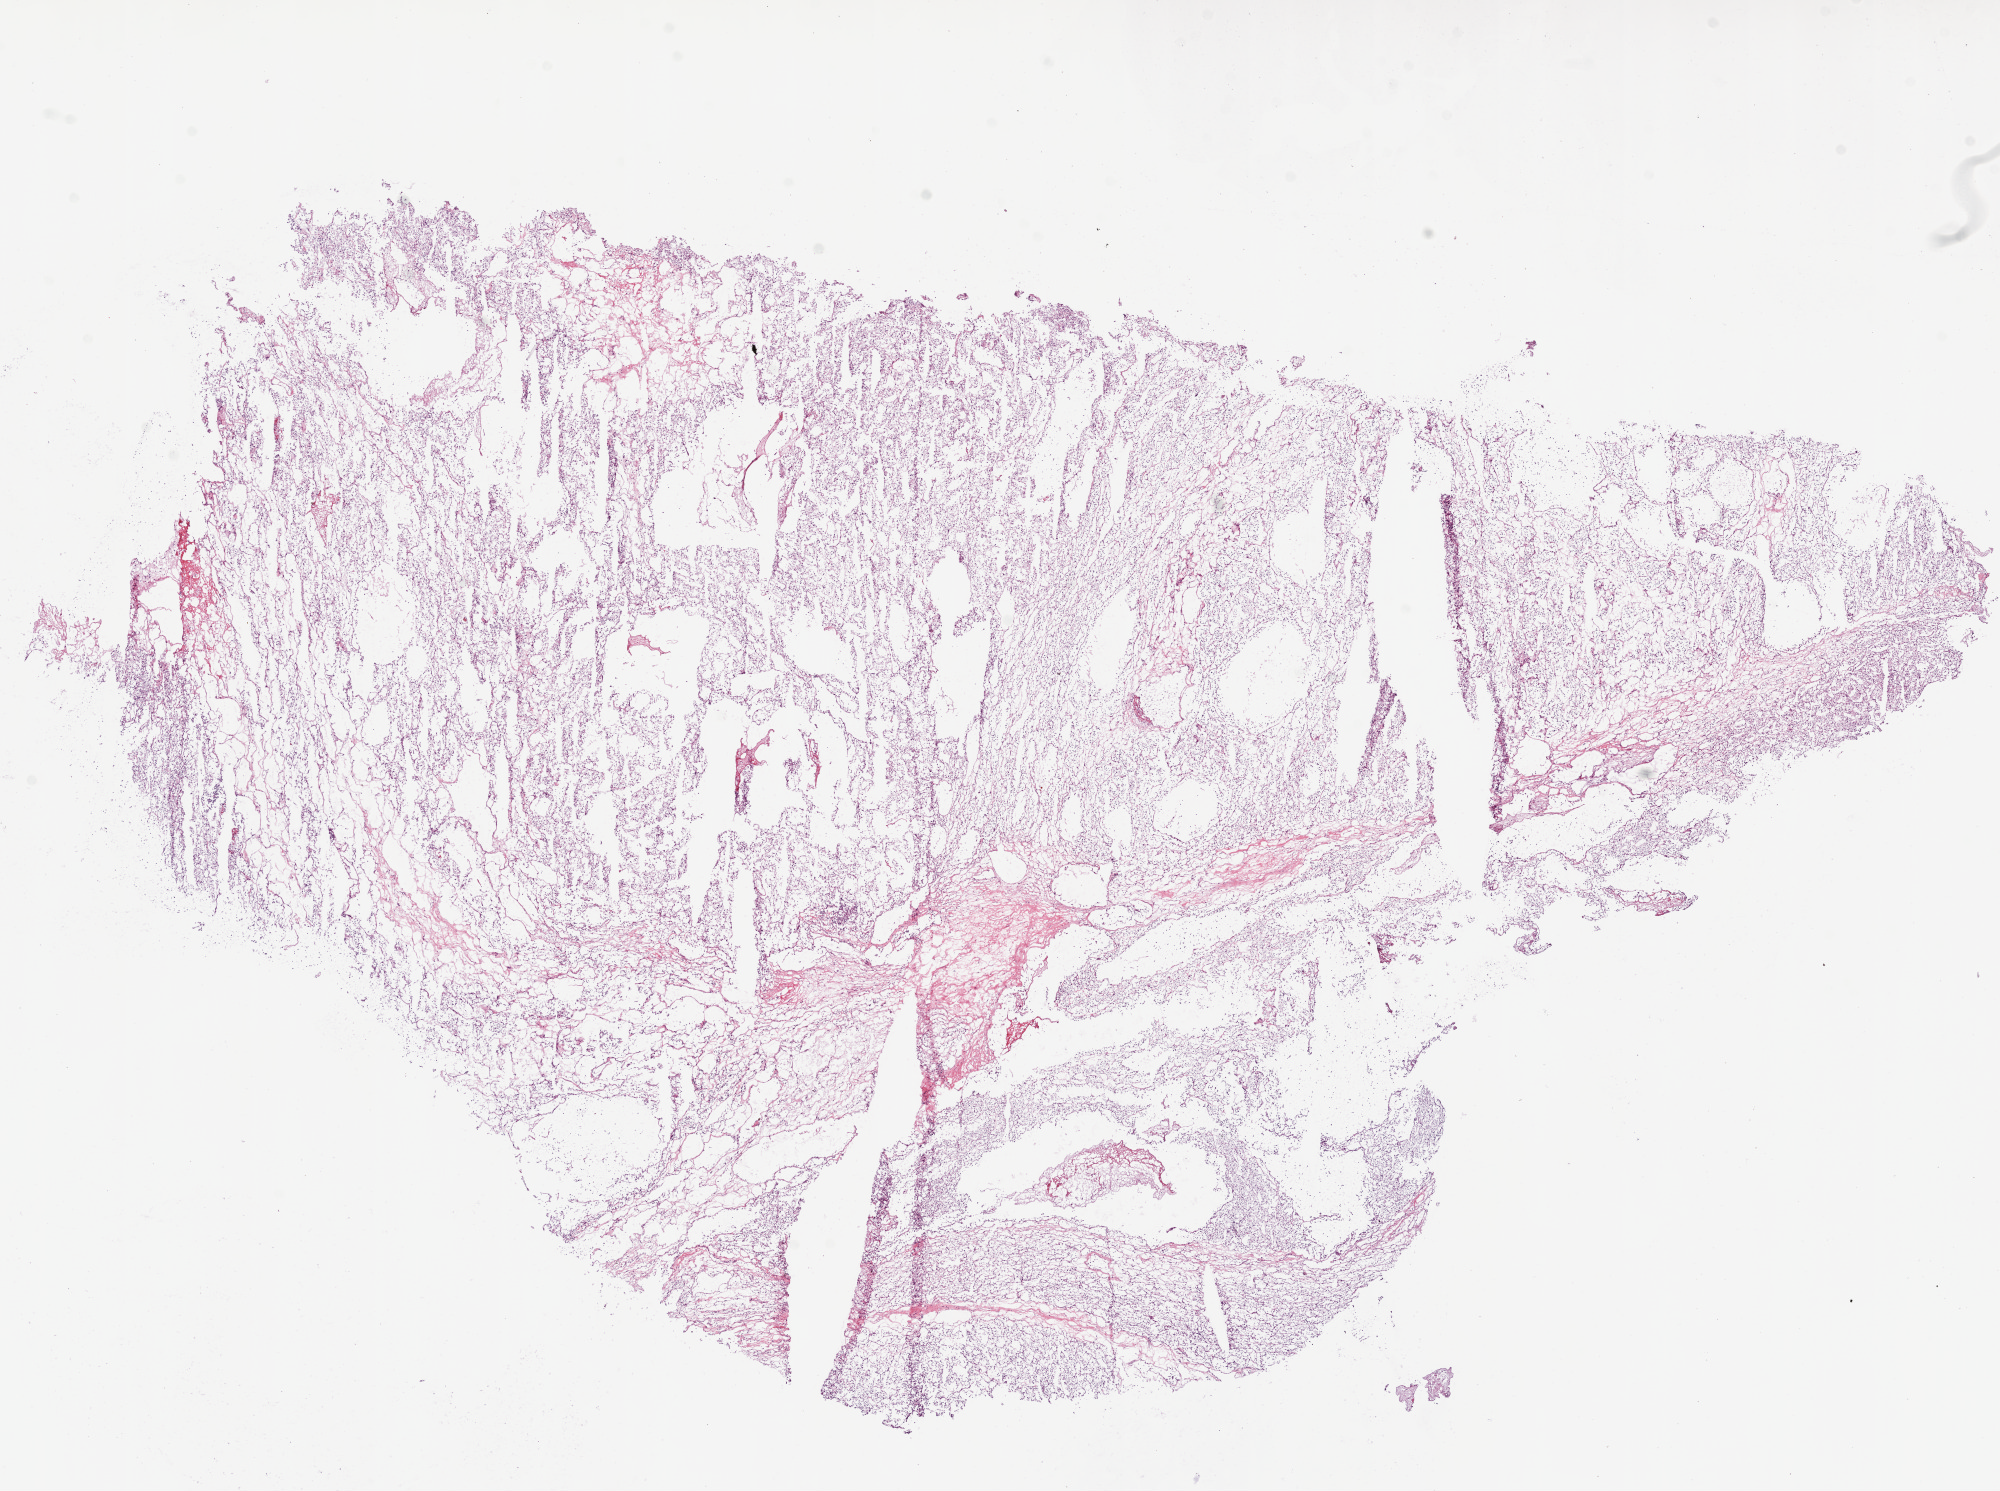
Whole-slide histology image, H&E-stained — whole scanned area (about 16.0 x 12.0 mm) shown as a low-resolution overview, frozen section from the bottom of the tissue portion, primary tumour sample from the kidney. Female patient; age at initial diagnosis 54 years. Histologic grade: G2 (moderately differentiated). Pathologist review of this section (percent, as recorded): tumour cells 90%, tumour nuclei 85%, normal cells 0%, stromal cells 10%, necrosis 0%.
Histologic diagnosis: Clear cell adenocarcinoma, NOS. TNM: T1a N0 M0. Laterality: right. AJCC pathologic stage: I. Lymph nodes positive (case pathology): 0 of 11 examined.